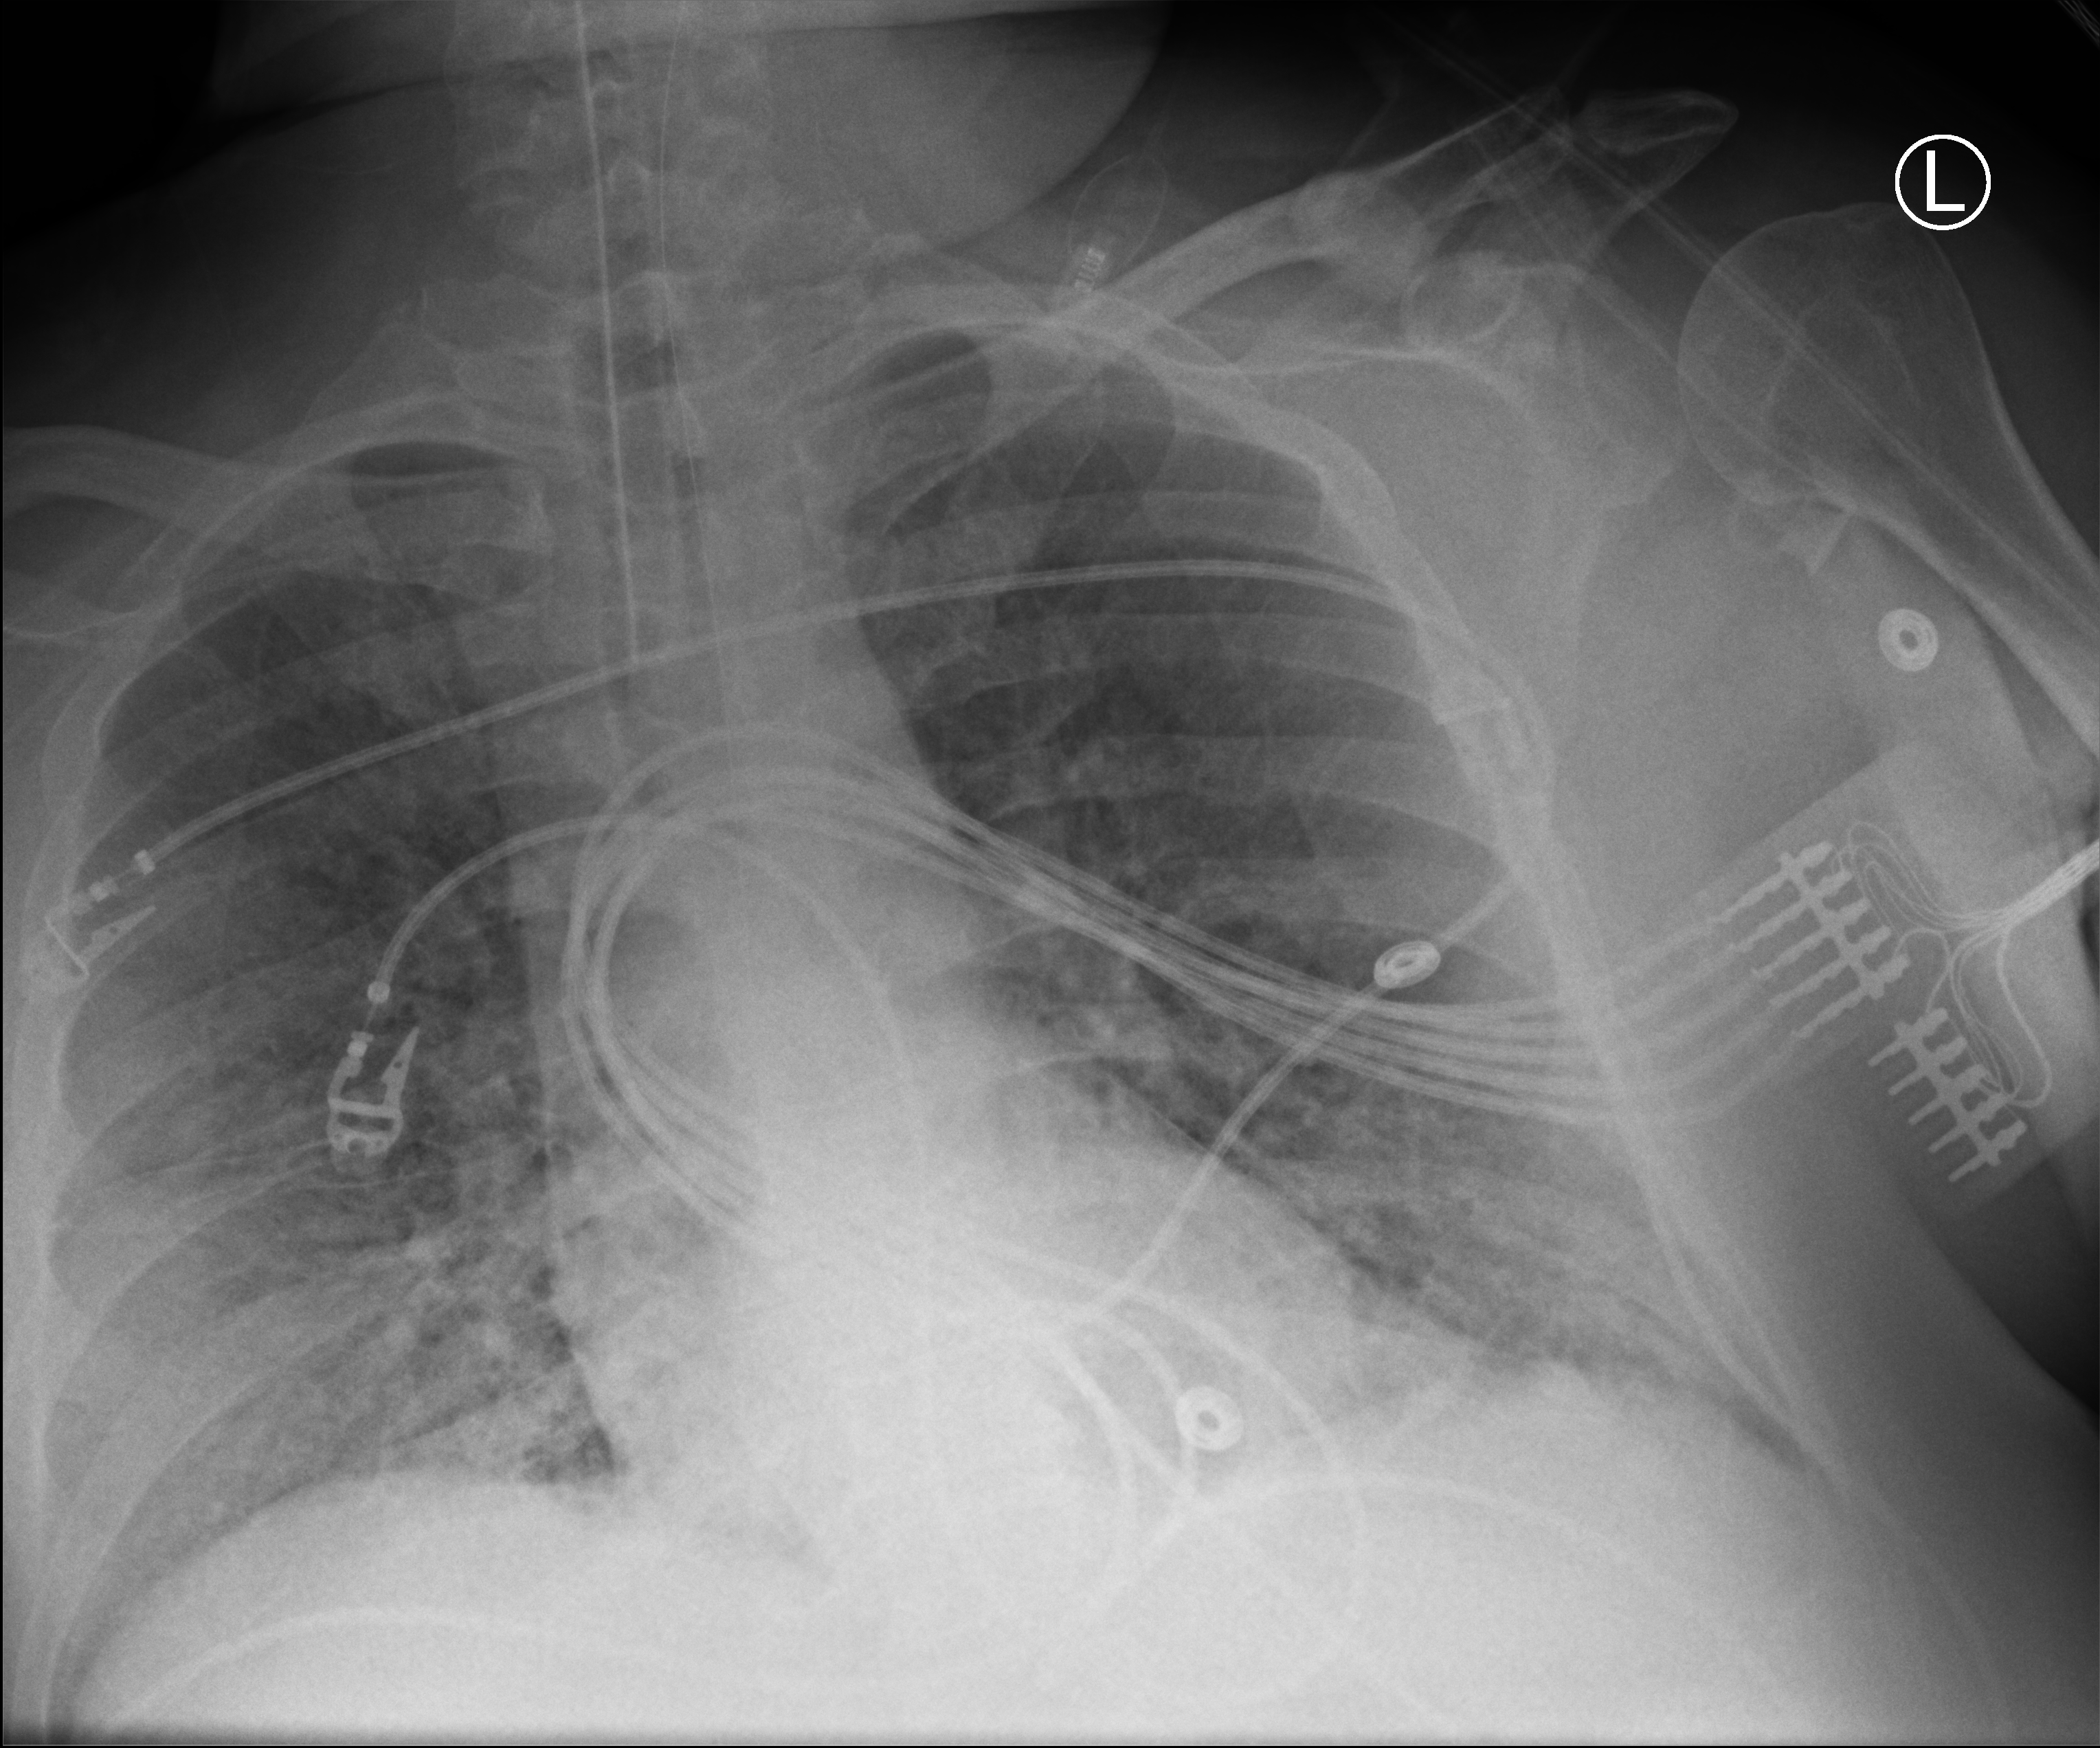
Portable chest radiograph, anteroposterior (AP) projection. Adult patient hospitalised with COVID-19, age 18–59 years.
From the hospital-stay record, not from the radiograph (when in the stay this image was taken is not recorded): chronic kidney disease (admission record): no; mechanically ventilated during this hospital stay: yes.